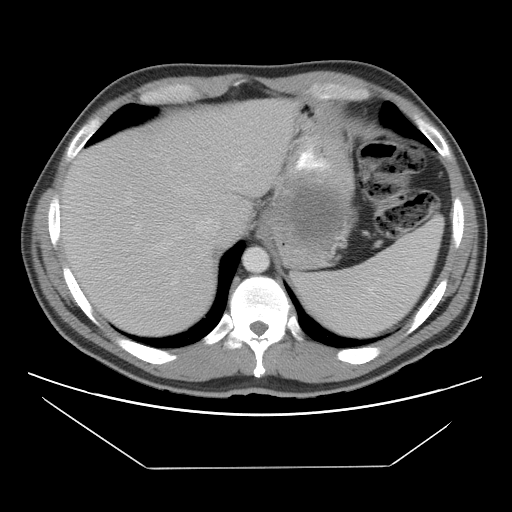
Contrast-enhanced abdominal CT, one axial slice; position 82 of 131 along the scan axis; soft-tissue window (W 400 / L 40 HU); 5 mm slice thickness; 512 × 512 image matrix, field of view 396 × 396 mm. Male patient, age 44 years. From the clinical record (not read from this slice): diagnosis: adrenocortical carcinoma; tumour side: left adrenal; tumour size at pathology: 15.5 cm; Ki-67 index: 6 %; stage (as recorded): 2.
Structures marked on this image (semi-automatic segmentation, software-assisted and operator-edited):
- mass: bounding box (x1, y1, x2, y2) in pixels: (291, 190, 338, 246)